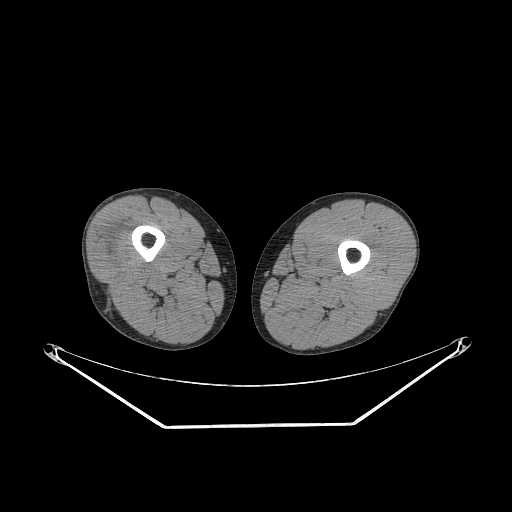
CT of an extremity soft-tissue mass (from a PET/CT study), one axial slice; position 221 of 267 along the scan axis; reconstruction kernel STANDARD; 140 kVp; soft-tissue window (W 400 / L 40 HU); 3.75 mm slice thickness; 512 × 512 image matrix, field of view 500 × 500 mm. Male patient. From the clinical record (not read from this slice): histological type: poorly differentiated synovial sarcoma; grade: high; site of the primary tumour: right buttock.
Structures marked on this image (expert contour drawn on MRI and transferred to this co-registered scan by the dataset authors):
- gross tumour volume including surrounding oedema: box from (x=100, y=235) to (x=134, y=270) px